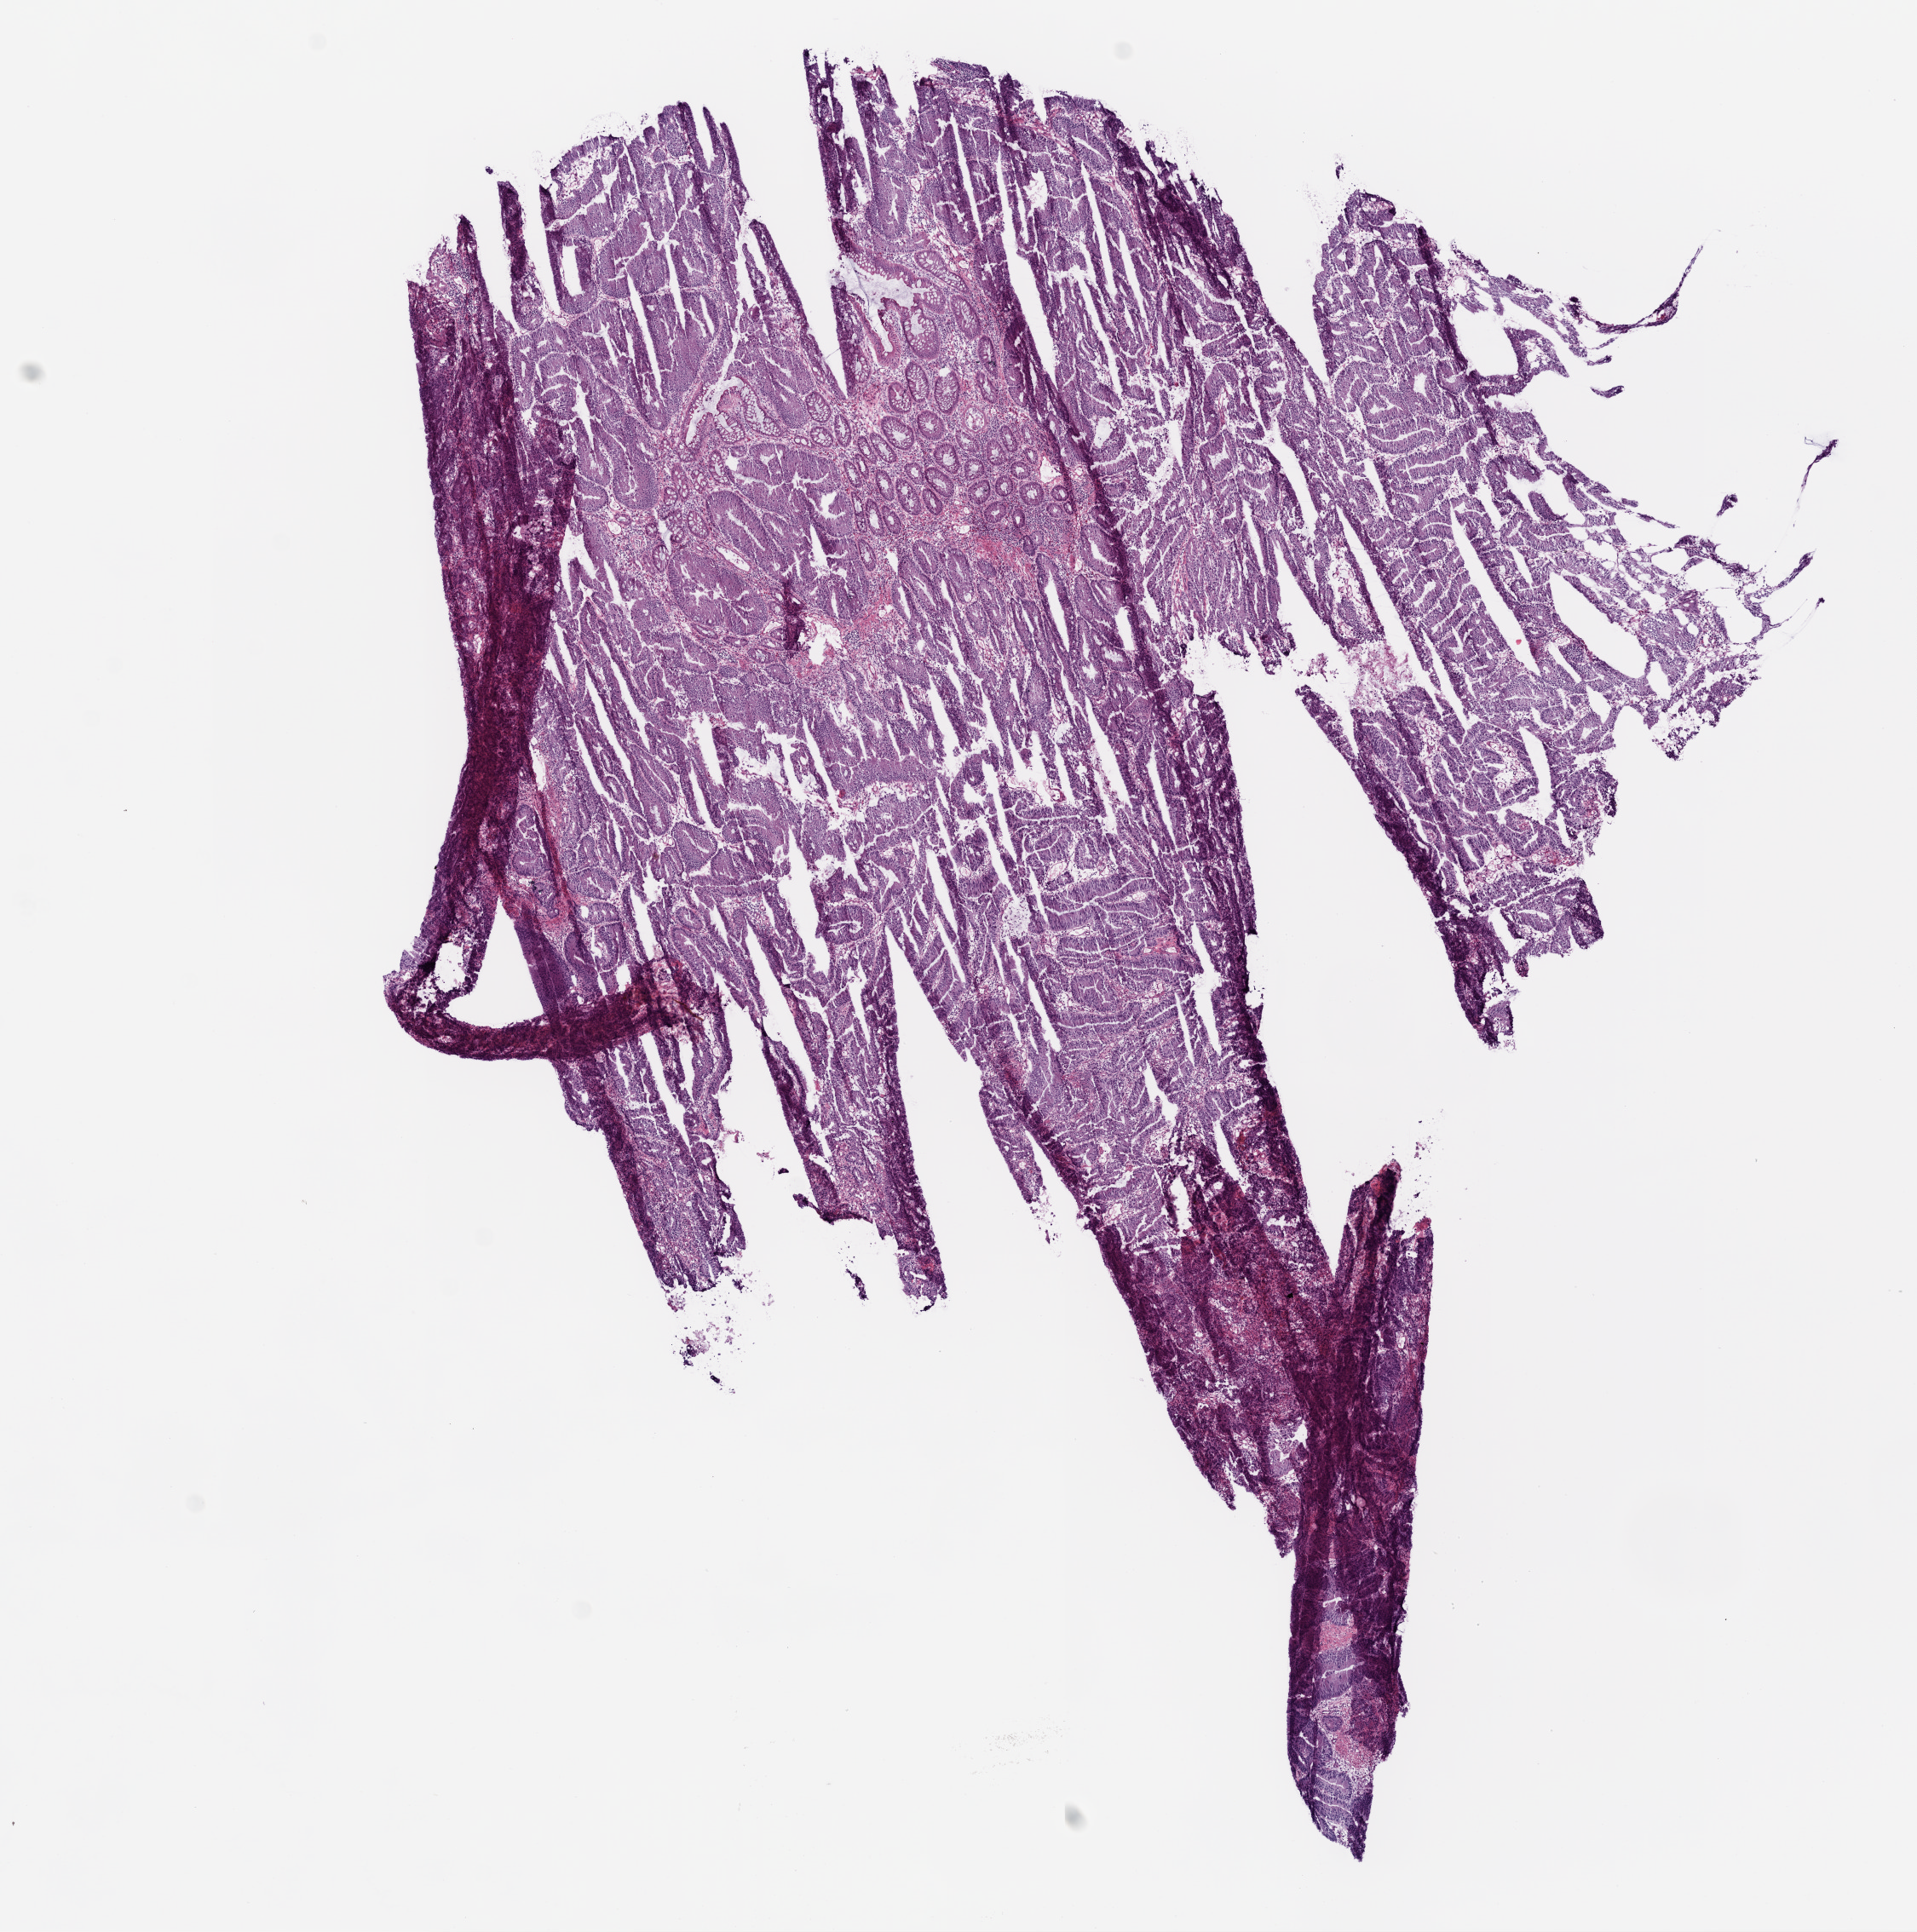
Digitized Hematoxylin and eosin (H&E) stained tissue section (whole slide), shown as a low-resolution overview of the whole scanned area (about 9.0 x 9.1 mm); frozen section from the top of the tissue portion; colon, primary tumour sample. Patient: female, age at initial diagnosis 72 years. Composition of this section per pathologist review: tumour cells 90%, tumour nuclei 90%, normal cells 0%, stromal cells 10%, necrosis 0%.
Histologic diagnosis: Adenocarcinoma, NOS. TNM: T3 N2 M0. Lymph nodes positive (case pathology): 5 of 25 examined. AJCC pathologic stage: IIIC (6th edition).